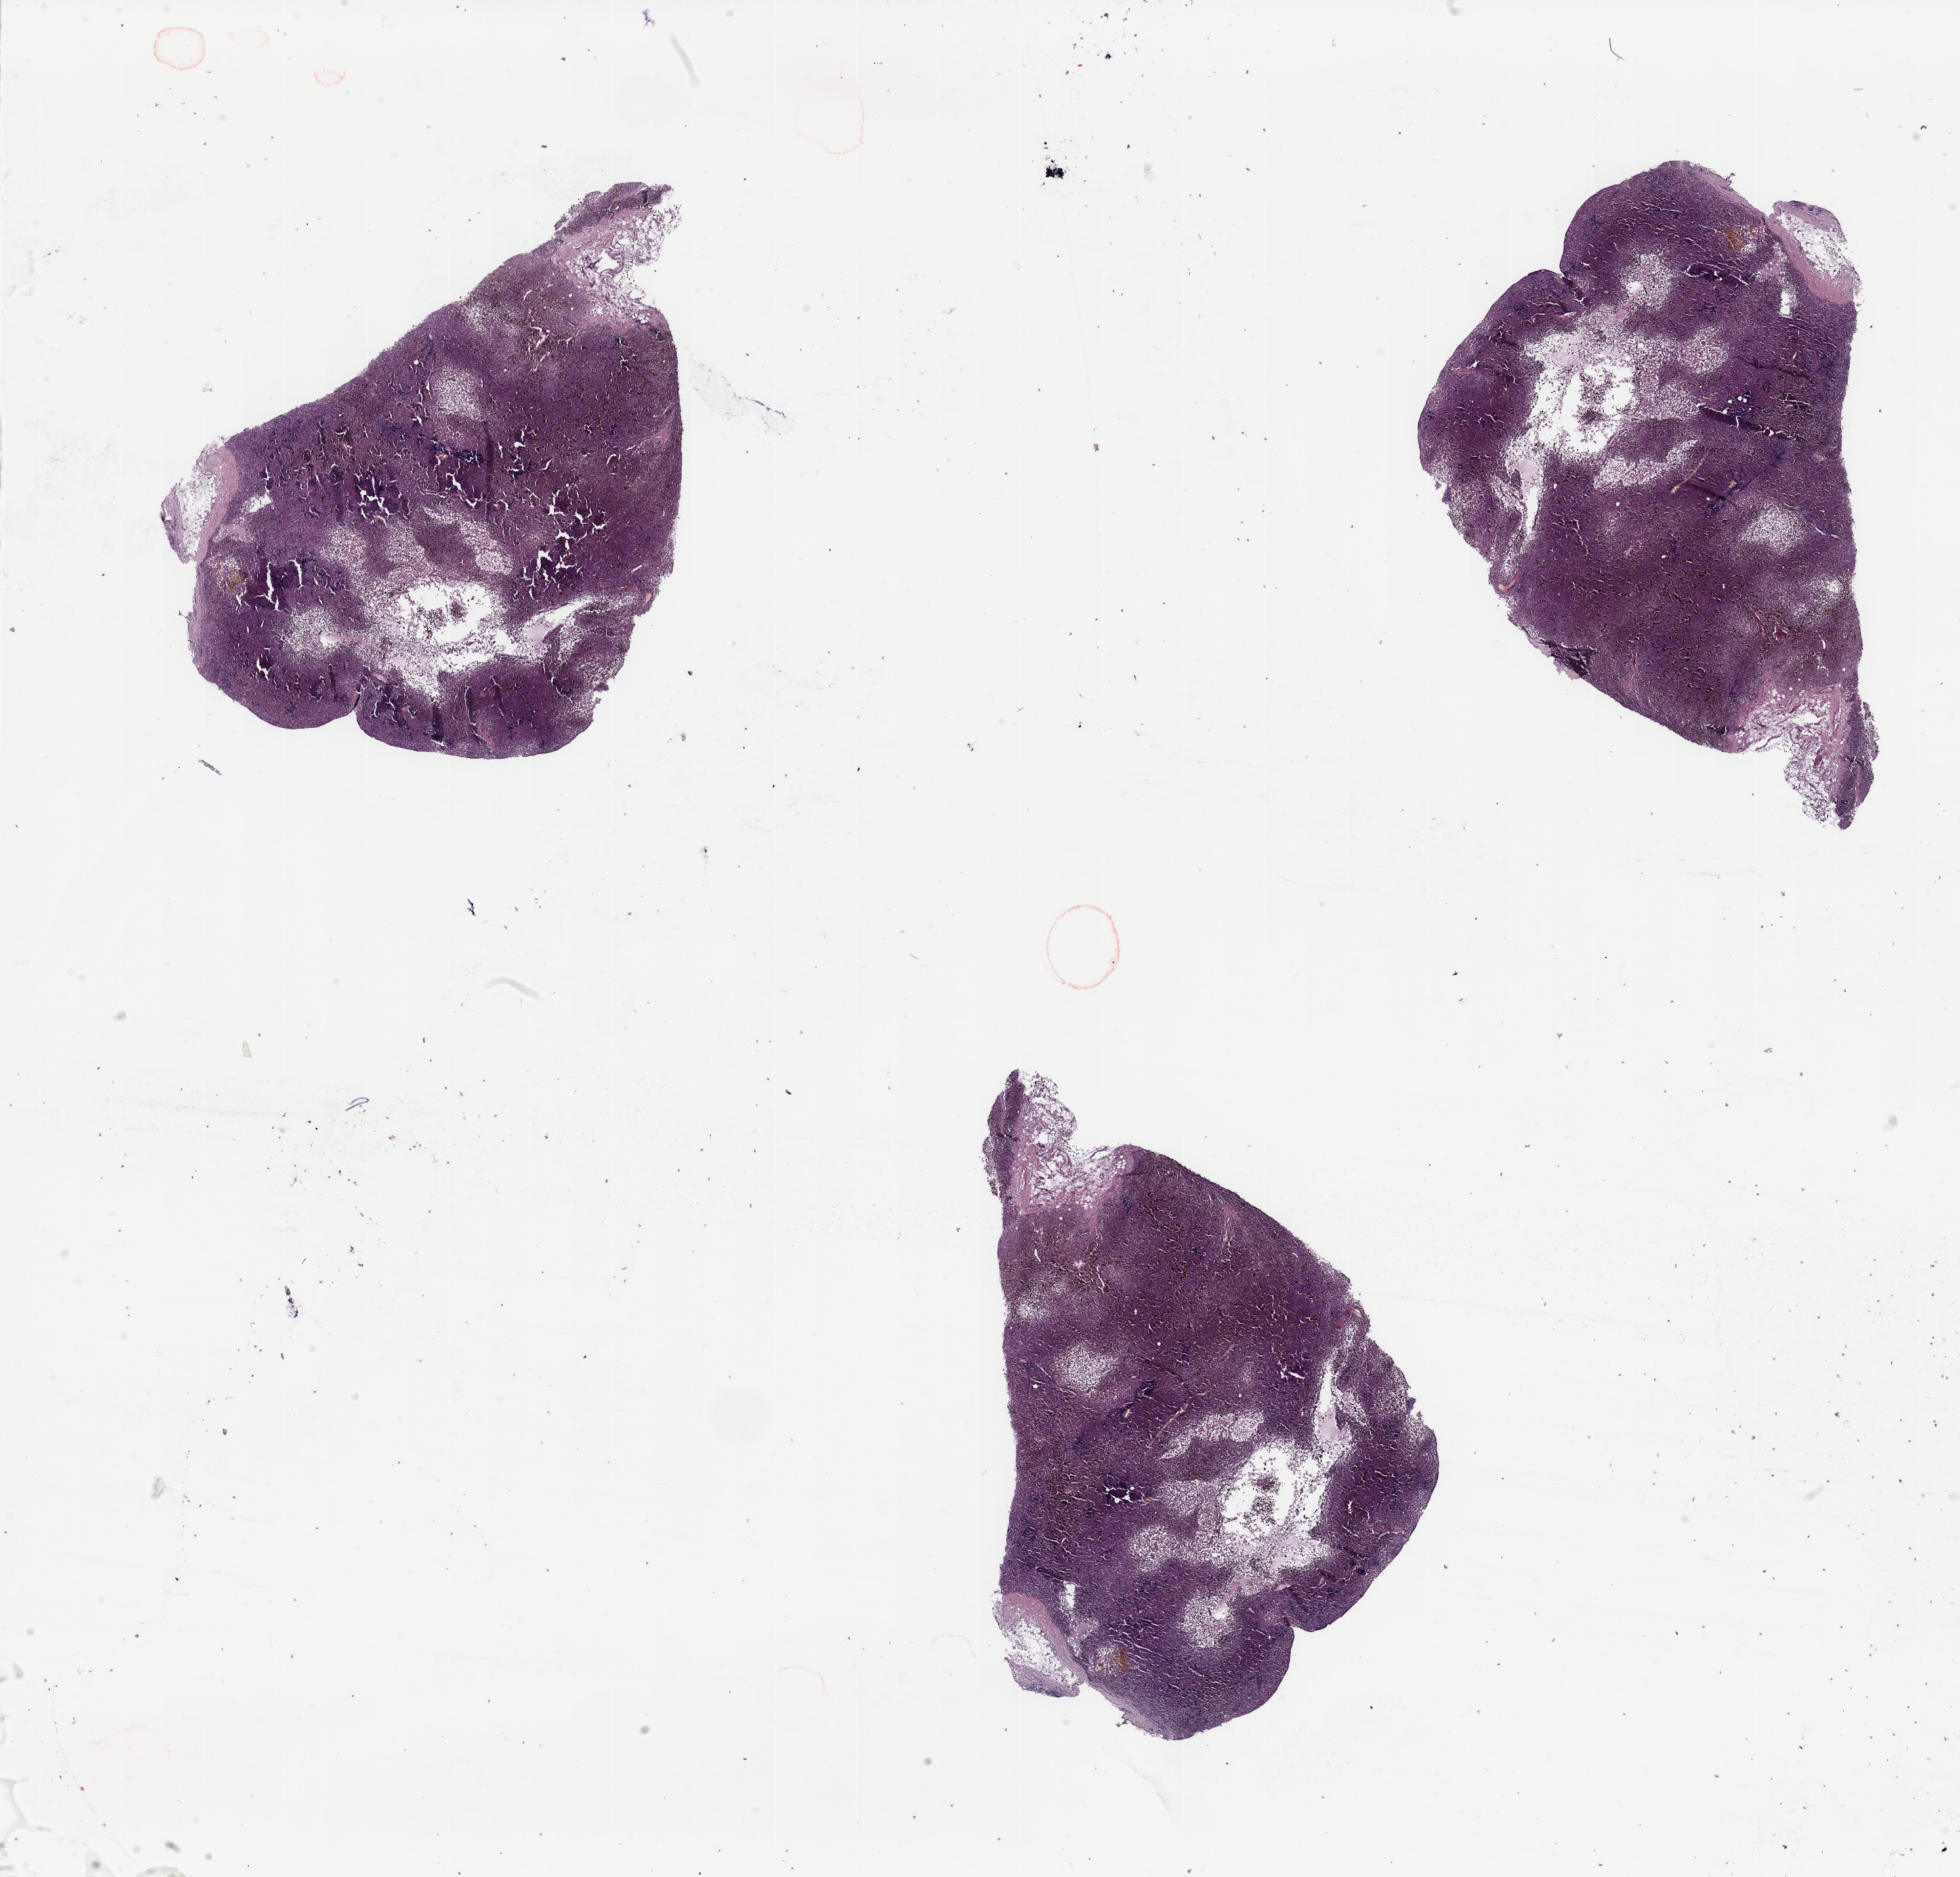
Digitized H&E-stained tissue section (whole slide) — a low-resolution overview of the entire scanned area, about 23.6 x 22.6 mm (slide scanned at 20x); melanoma tumour tissue; sampled site not recorded. Patient: female, age 51 years.
Primary tumour site (as recorded): trunk. Histologic diagnosis: Malignant melanoma, NOS. AJCC pathologic stage: IB.